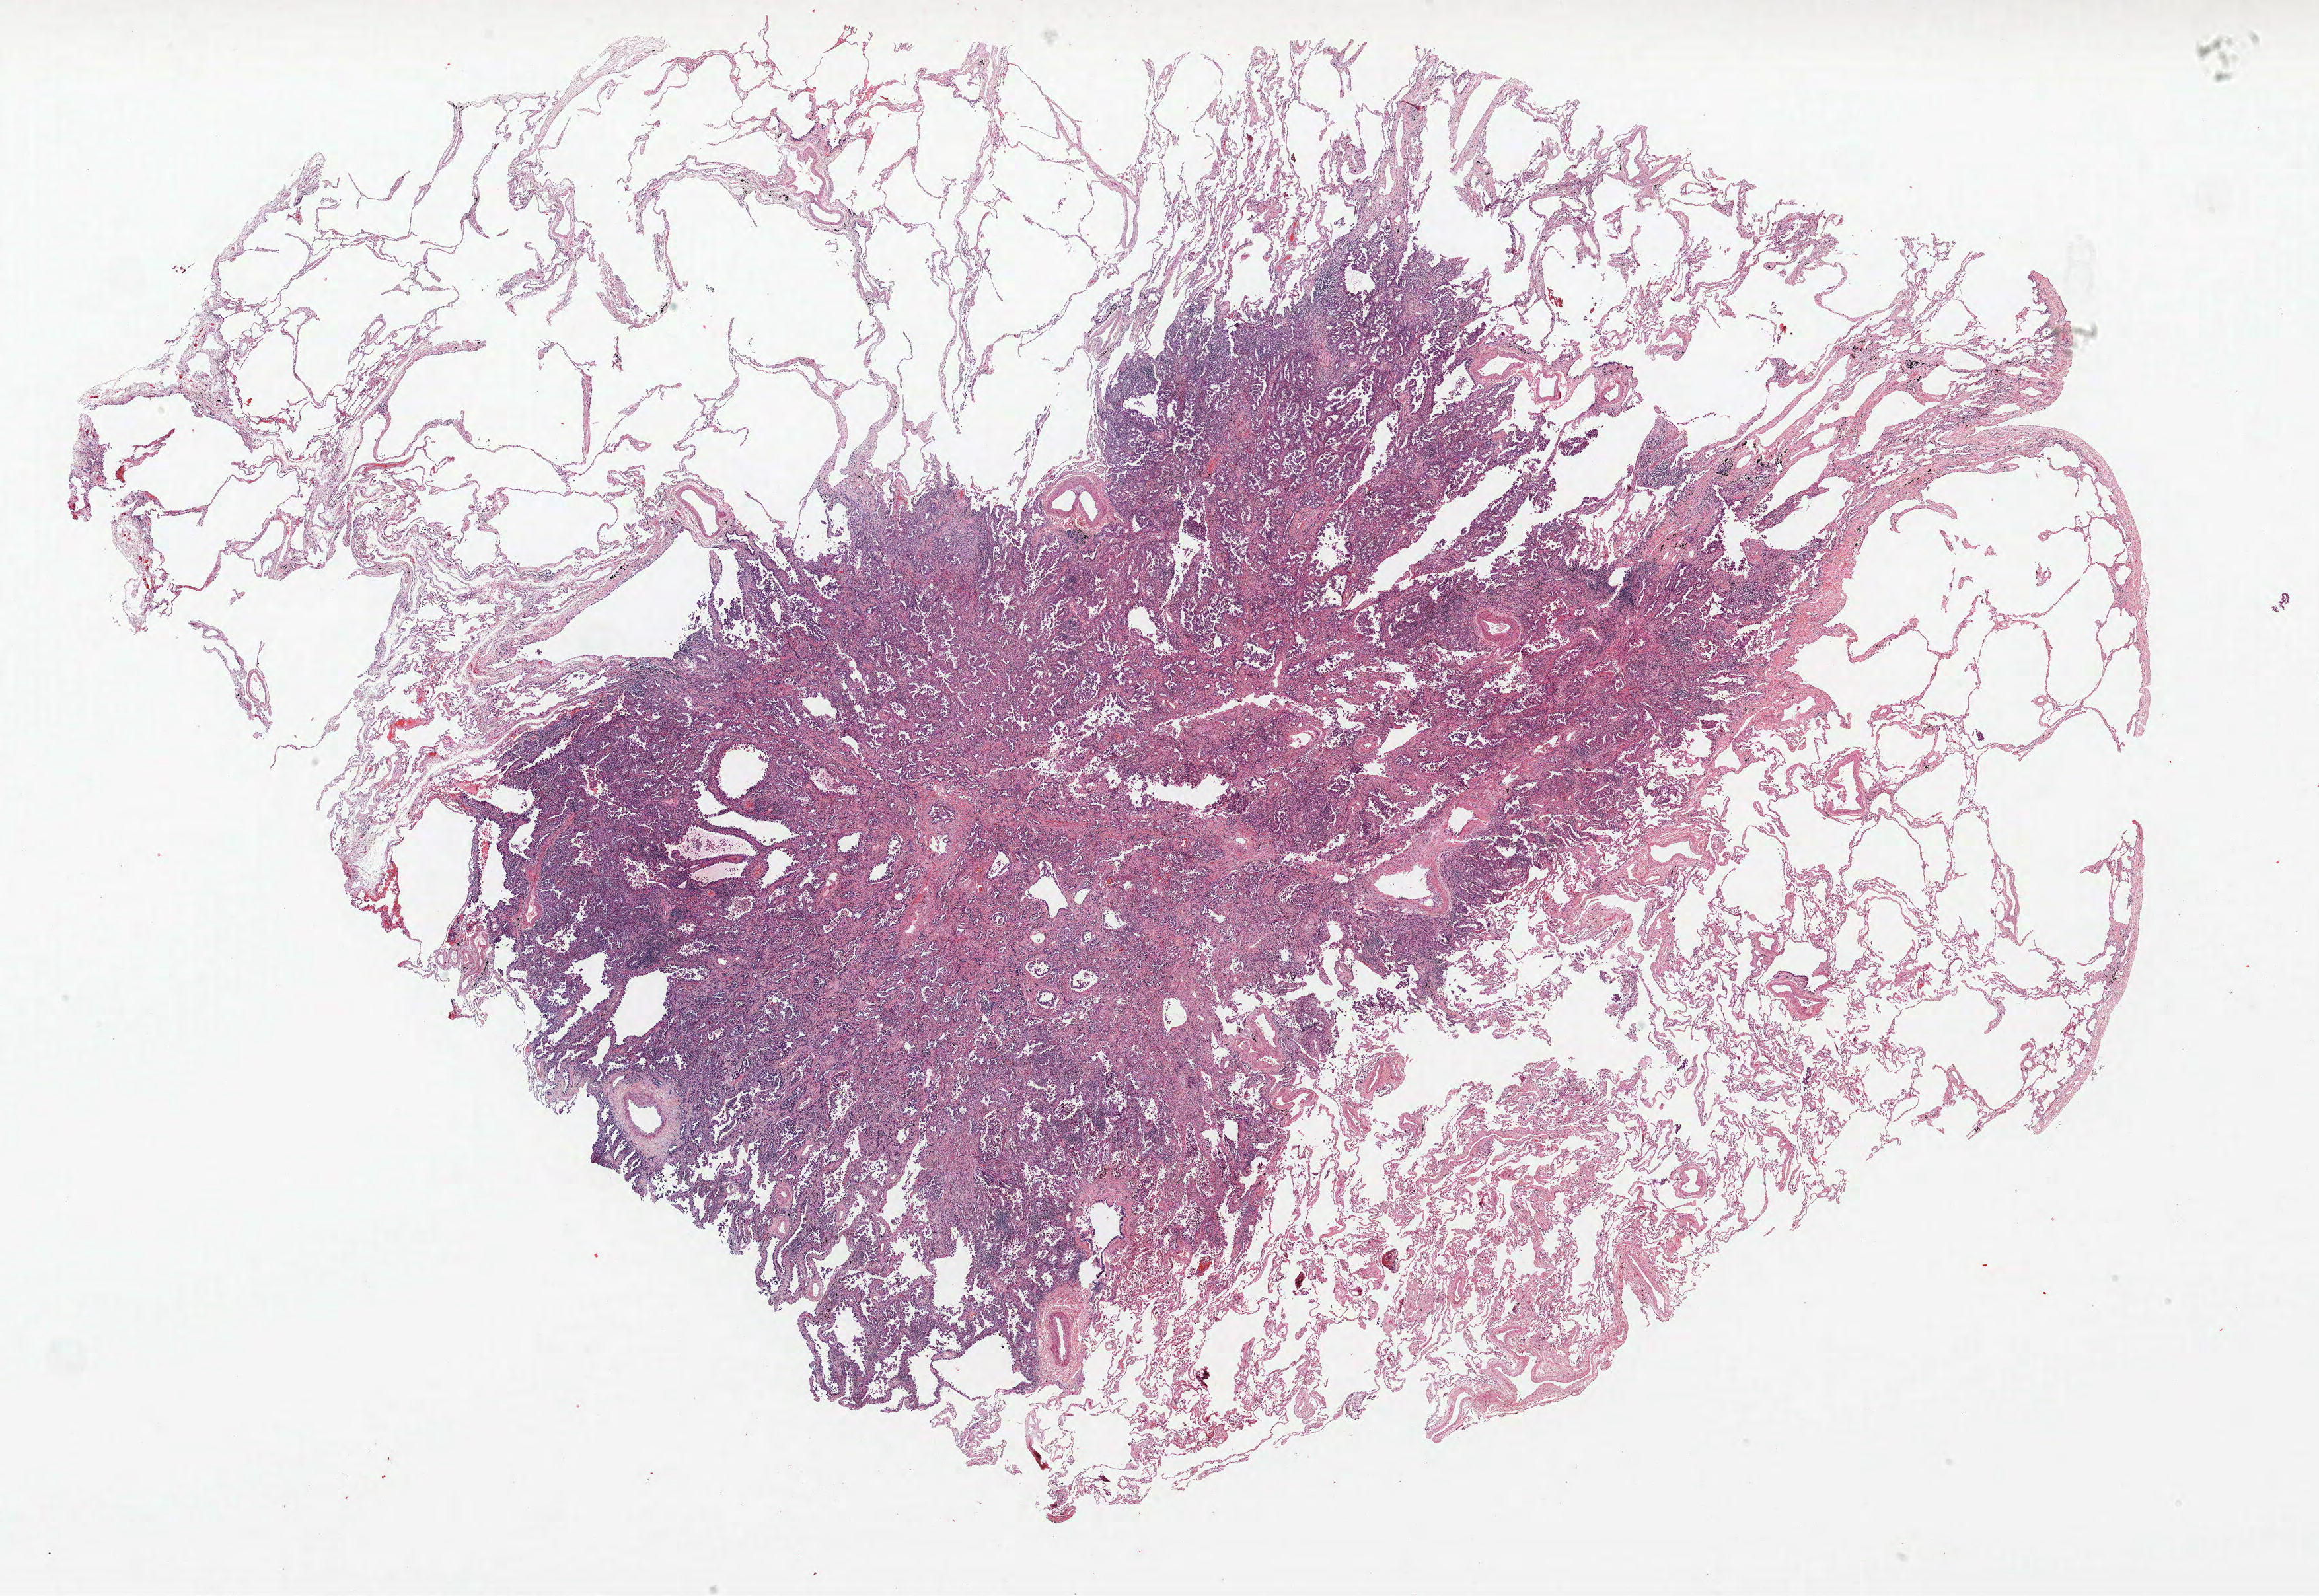
Whole-slide histology image, Hematoxylin and eosin (H&E) stained, low-resolution overview of the scanned area, about 28.1 x 19.3 mm (acquisition: 40x scan). FFPE section. Lung. Male, age 65 at enrolment. Former smoker at enrolment. Grade: moderately differentiated (G2).
- tumour size (pathology): 14 mm
- participant's lung-cancer diagnosis: Bronchiolo-alveolar adenocarcinoma, NOS
- stage (AJCC 6th edition): IIA
- primary tumour location (clinical record): right upper lobe